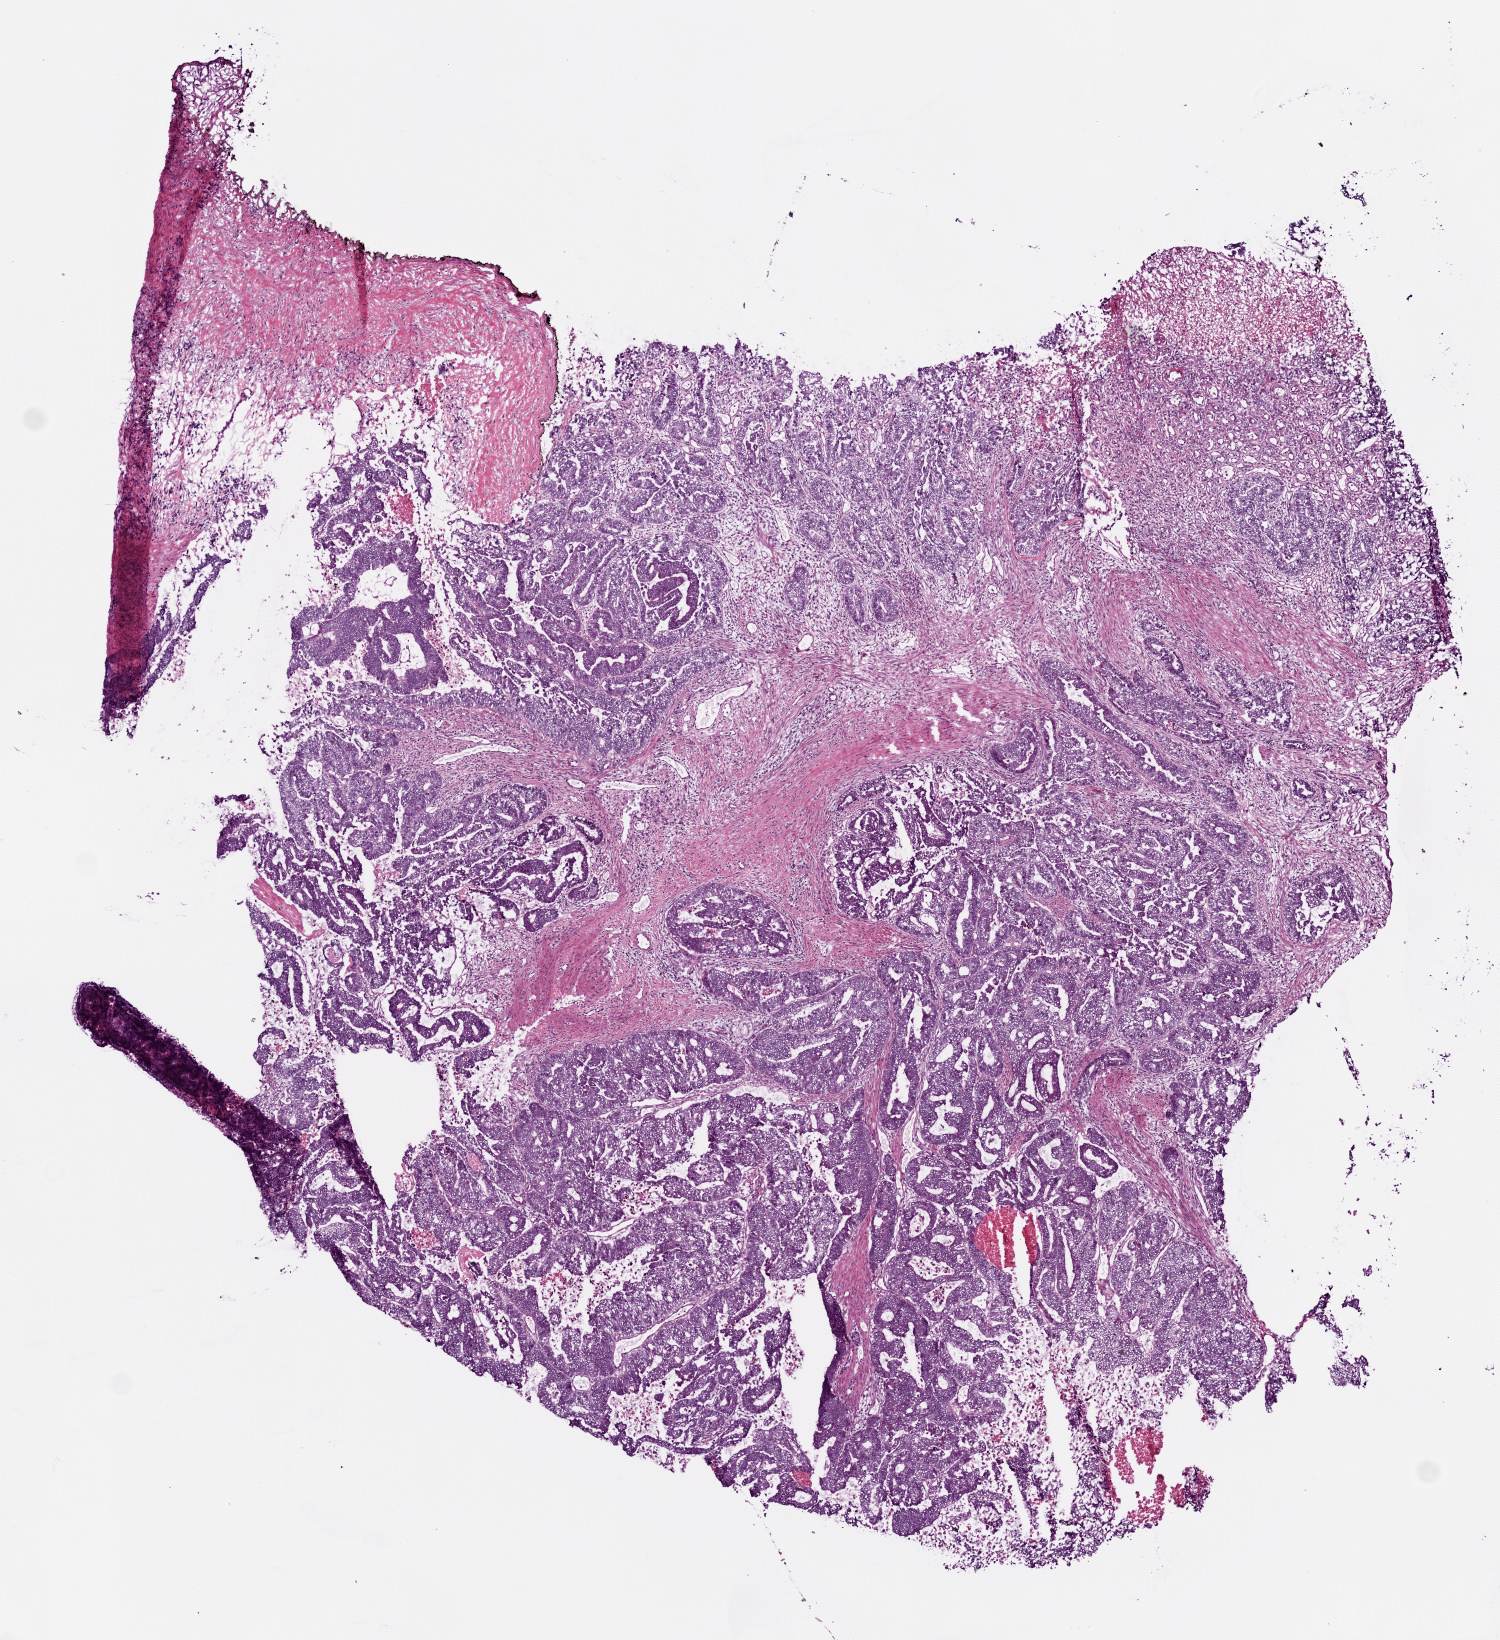
Whole-slide histology image, H&E — a low-resolution overview of the entire scanned area, about 6.0 x 6.6 mm, frozen section from the top of the tissue portion, colon, primary tumour sample. Male patient; age at initial diagnosis 82 years. Slide review estimates, as recorded: tumour cells 87%, tumour nuclei 80%, normal cells 11%, stromal cells 0%, necrosis 2%. Inflammatory infiltration, as recorded: lymphocyte infiltration 10%, monocyte infiltration 1%, neutrophil infiltration 1%.
Lymph nodes positive (case pathology): 0 of 26 examined. AJCC pathologic stage: I. Diagnosis: Adenocarcinoma, NOS.